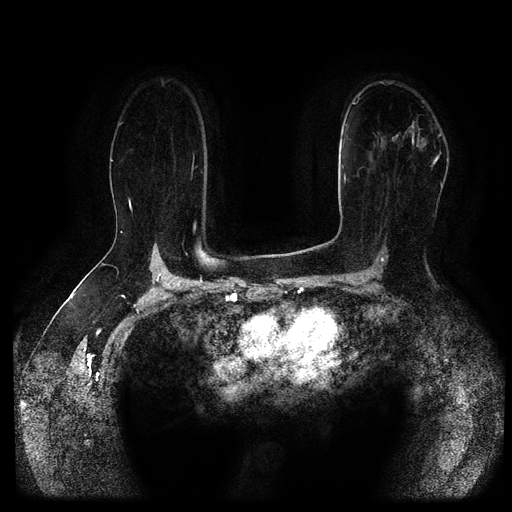
Breast MRI (dynamic contrast-enhanced, multi-phase), one axial slice; position 69 of 116 along the scan axis; dynamic contrast-enhanced series, time point 2 of 5 at this slice position (early post-contrast); 1.5 T; TE 2.6 ms, TR 5.3 ms; 2 mm slice thickness; 512 × 512 image matrix, field of view 360 × 360 mm. Patient: female, 67 years.
Outlined on this slice (semi-automatically segmented with operator editing):
- breast lesion (labelled 'tumour' in the annotation; benign lesions carry a separate 'benign' label): bounding box (x1, y1, x2, y2) in pixels: (389, 125, 412, 147)